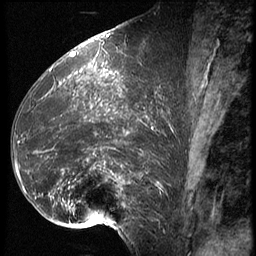
Breast MRI (dynamic contrast-enhanced), one sagittal slice; position 30 of 62 along the scan axis; 3 images stored at this slice position (order not interpretable as contrast timing); 1.5 T; TE 4.2 ms, TR 9 ms; 2.5 mm slice thickness; 256 × 256 image matrix, field of view 180 × 180 mm. Patient: female, 39 years. From the clinical record (not read from this slice): setting: breast cancer imaged before/during neoadjuvant chemotherapy; receptor status: HER2-positive.
Structures marked on this image (semi-automatically segmented with operator editing):
- analysis volume of interest (the breast-tissue region the enhancement analysis was run in; not a lesion): bounding box [x1, y1, x2, y2] px = [16, 64, 171, 228]
- tumour enhancement mask (voxels above the 140 % enhancement threshold inside the analysis volume of interest): [16, 72, 169, 225]